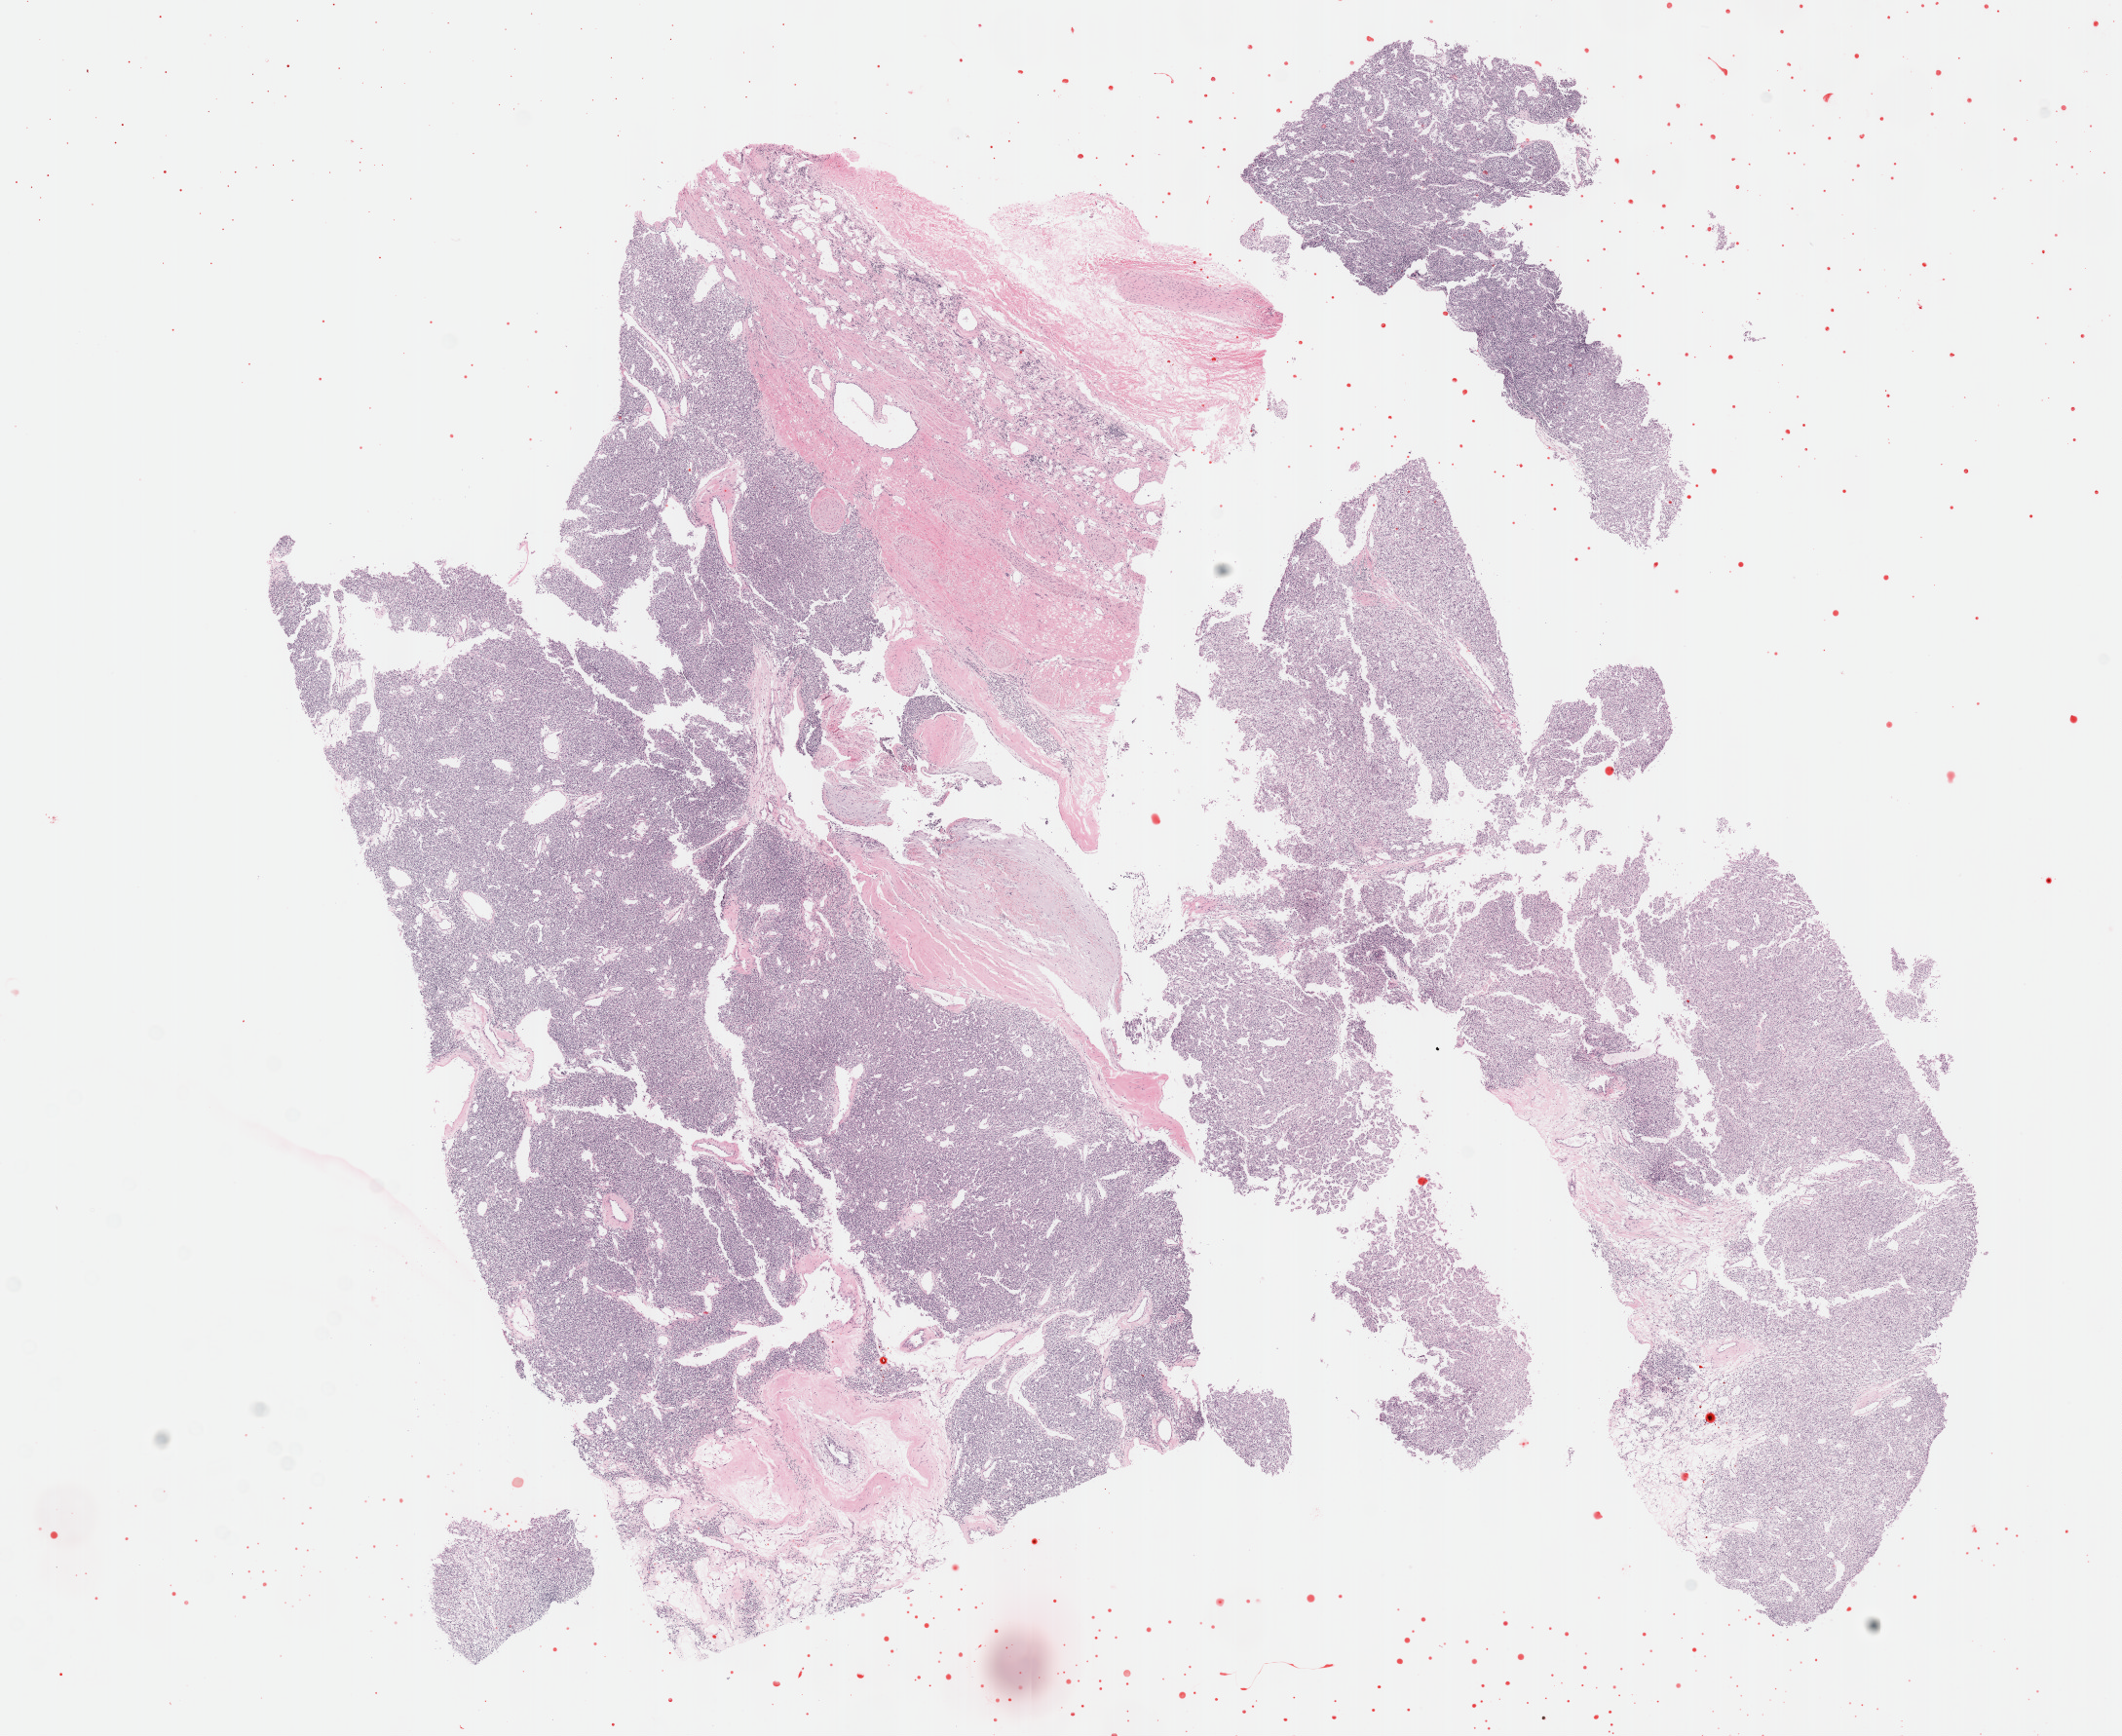
Whole-slide histology image, Hematoxylin and eosin (H&E) stained — a low-resolution overview of the entire scanned area, about 17.6 x 14.4 mm, formalin-fixed paraffin-embedded (FFPE) diagnostic section, kidney, primary tumour sample. Patient: male, age at initial diagnosis 72 years. Histologic grade: G2 (moderately differentiated).
• diagnosis: Clear cell adenocarcinoma, NOS
• AJCC pathologic stage: I
• laterality: right